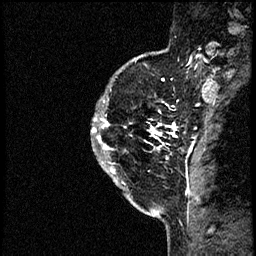
Breast MRI (dynamic contrast-enhanced), one sagittal slice. Position 47 of 60 along the scan axis. Dynamic contrast-enhanced study with each time point stored as its own series, time point 2 of 4 at this slice position (early post-contrast, ordered by acquisition time). 1.5 T. TE 4.2 ms, TR 17.6 ms. 2 mm slice thickness. 256 × 256 image matrix, field of view 200 × 200 mm. Patient: female, 40 years. From the clinical record (not read from this slice): setting: breast cancer imaged before/during neoadjuvant chemotherapy; receptor status: HER2-positive.
Structures marked on this image (semi-automatically segmented with operator editing):
- analysis volume of interest (the breast-tissue region the enhancement analysis was run in; not a lesion): bounding box [x1, y1, x2, y2] px = [92, 56, 197, 205]
- tumour enhancement mask (voxels above the 100 % enhancement threshold inside the analysis volume of interest): [92, 118, 197, 200]